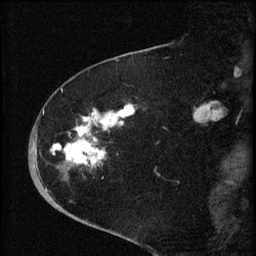
Breast MRI (dynamic contrast-enhanced), one sagittal slice; position 21 of 60 along the scan axis; dynamic contrast-enhanced series, image 2 of 4 at this slice position (ordered by acquisition); 1.5 T; TE 4.2 ms, TR 8.2 ms; 2 mm slice thickness; 256 × 256 image matrix, field of view 180 × 180 mm. Female patient, age 71 years.
Structures marked on this image (semi-automatic segmentation, software-assisted and operator-edited):
- analysis volume of interest (the breast-tissue region the enhancement analysis was run in; not a lesion): box from (x=35, y=75) to (x=142, y=190) px
- tumour enhancement mask (voxels above the 70 % enhancement threshold inside the analysis volume of interest): (x=43, y=104)–(x=135, y=167)